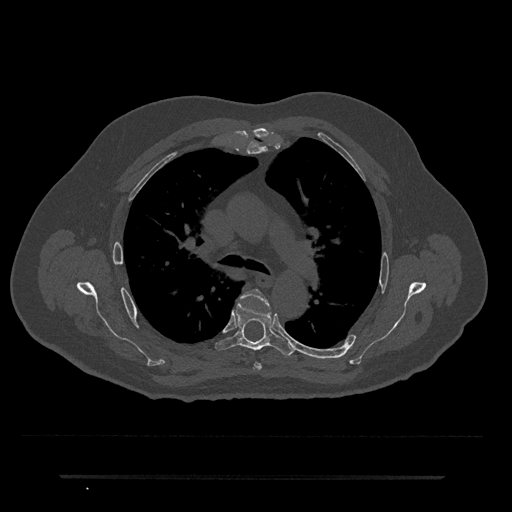
CT including the spine, one axial slice; slice 493 of 797 in the series (ordered by position); reconstruction kernel Br40s/3; 120 kVp; bone window (W 1800 / L 400 HU); 0.5 mm slice thickness; 512 × 512 image matrix. Male patient, age 69 years. From the clinical record (not read from this slice): primary cancer: prostate.
Structures marked on this image (semi-automatically segmented with operator editing):
- T4 vertebra: bounding box [x1, y1, x2, y2] px = [241, 289, 268, 370]
- T5 vertebra: [215, 300, 295, 355]